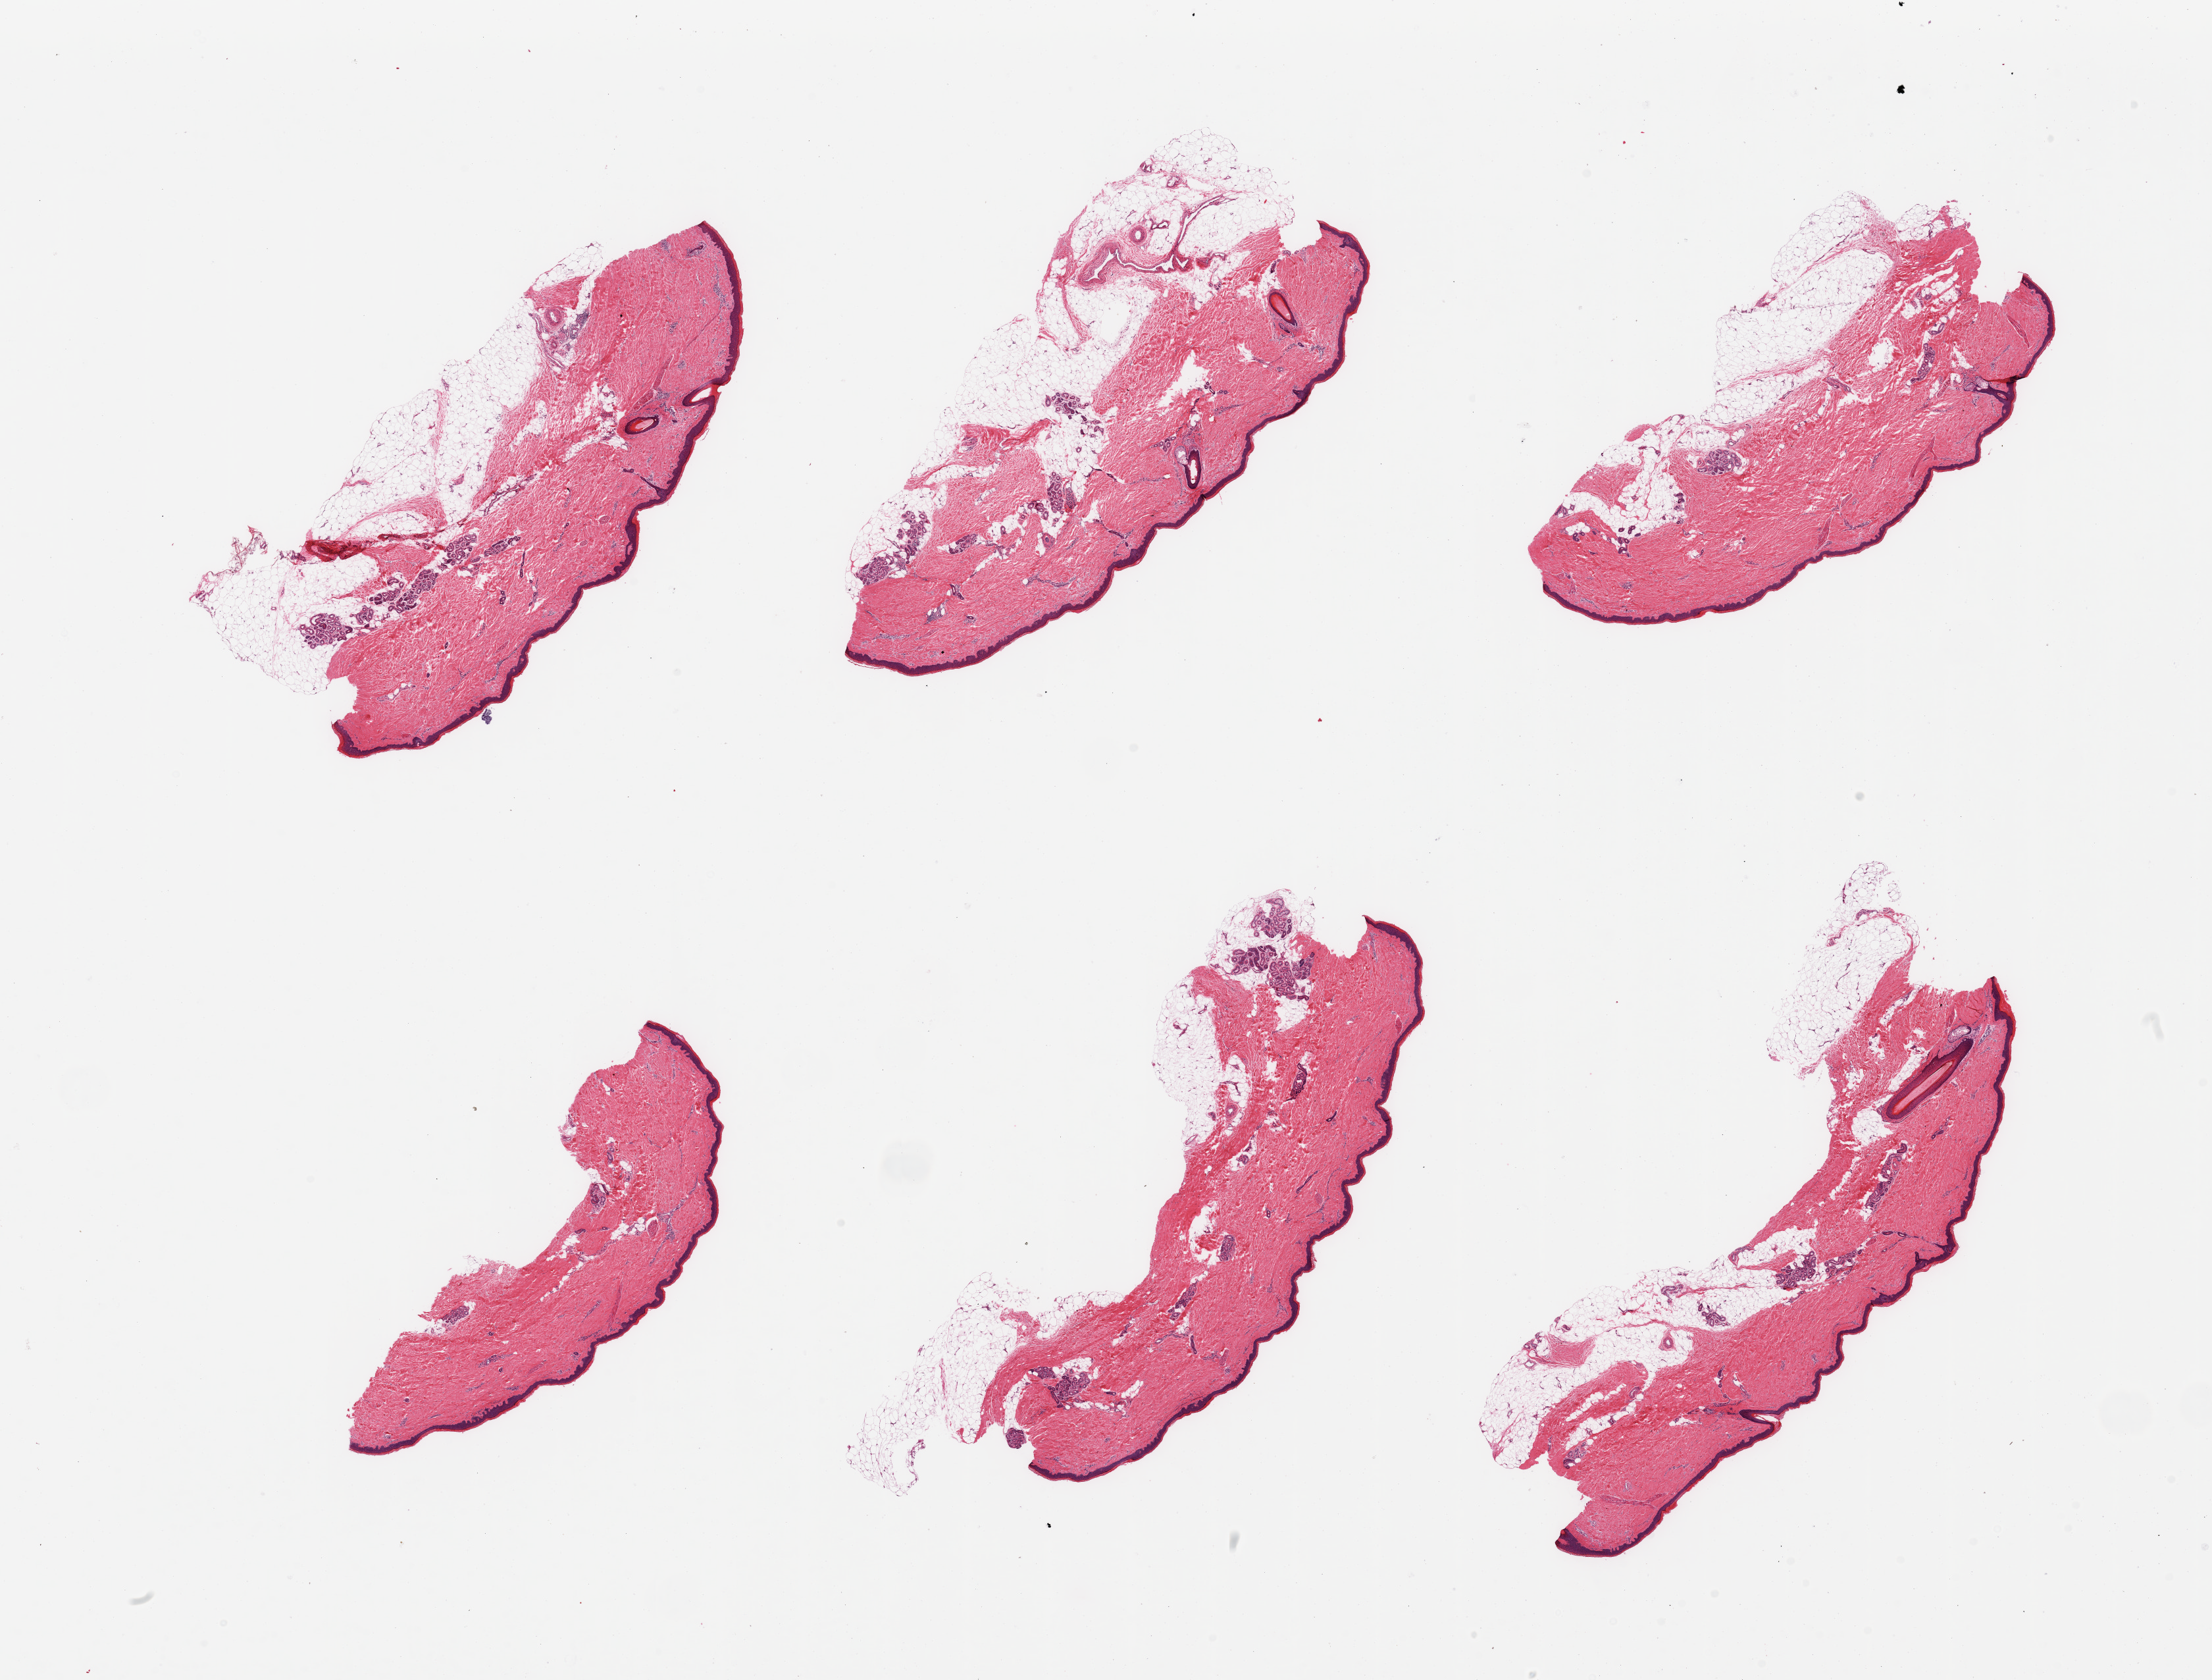
Whole-slide image, haematoxylin and eosin stain, a low-resolution overview of the entire scanned area, about 26.6 x 20.2 mm, PAXgene-fixed paraffin-embedded (PFPE) section, target tissue: skin of lower leg, tissue donor sample. Donor sex: male.
- review note (as recorded): 6 pieces; thick subcutaneous fat up to 1.6mm in 3 pieces; dermal fat 10%